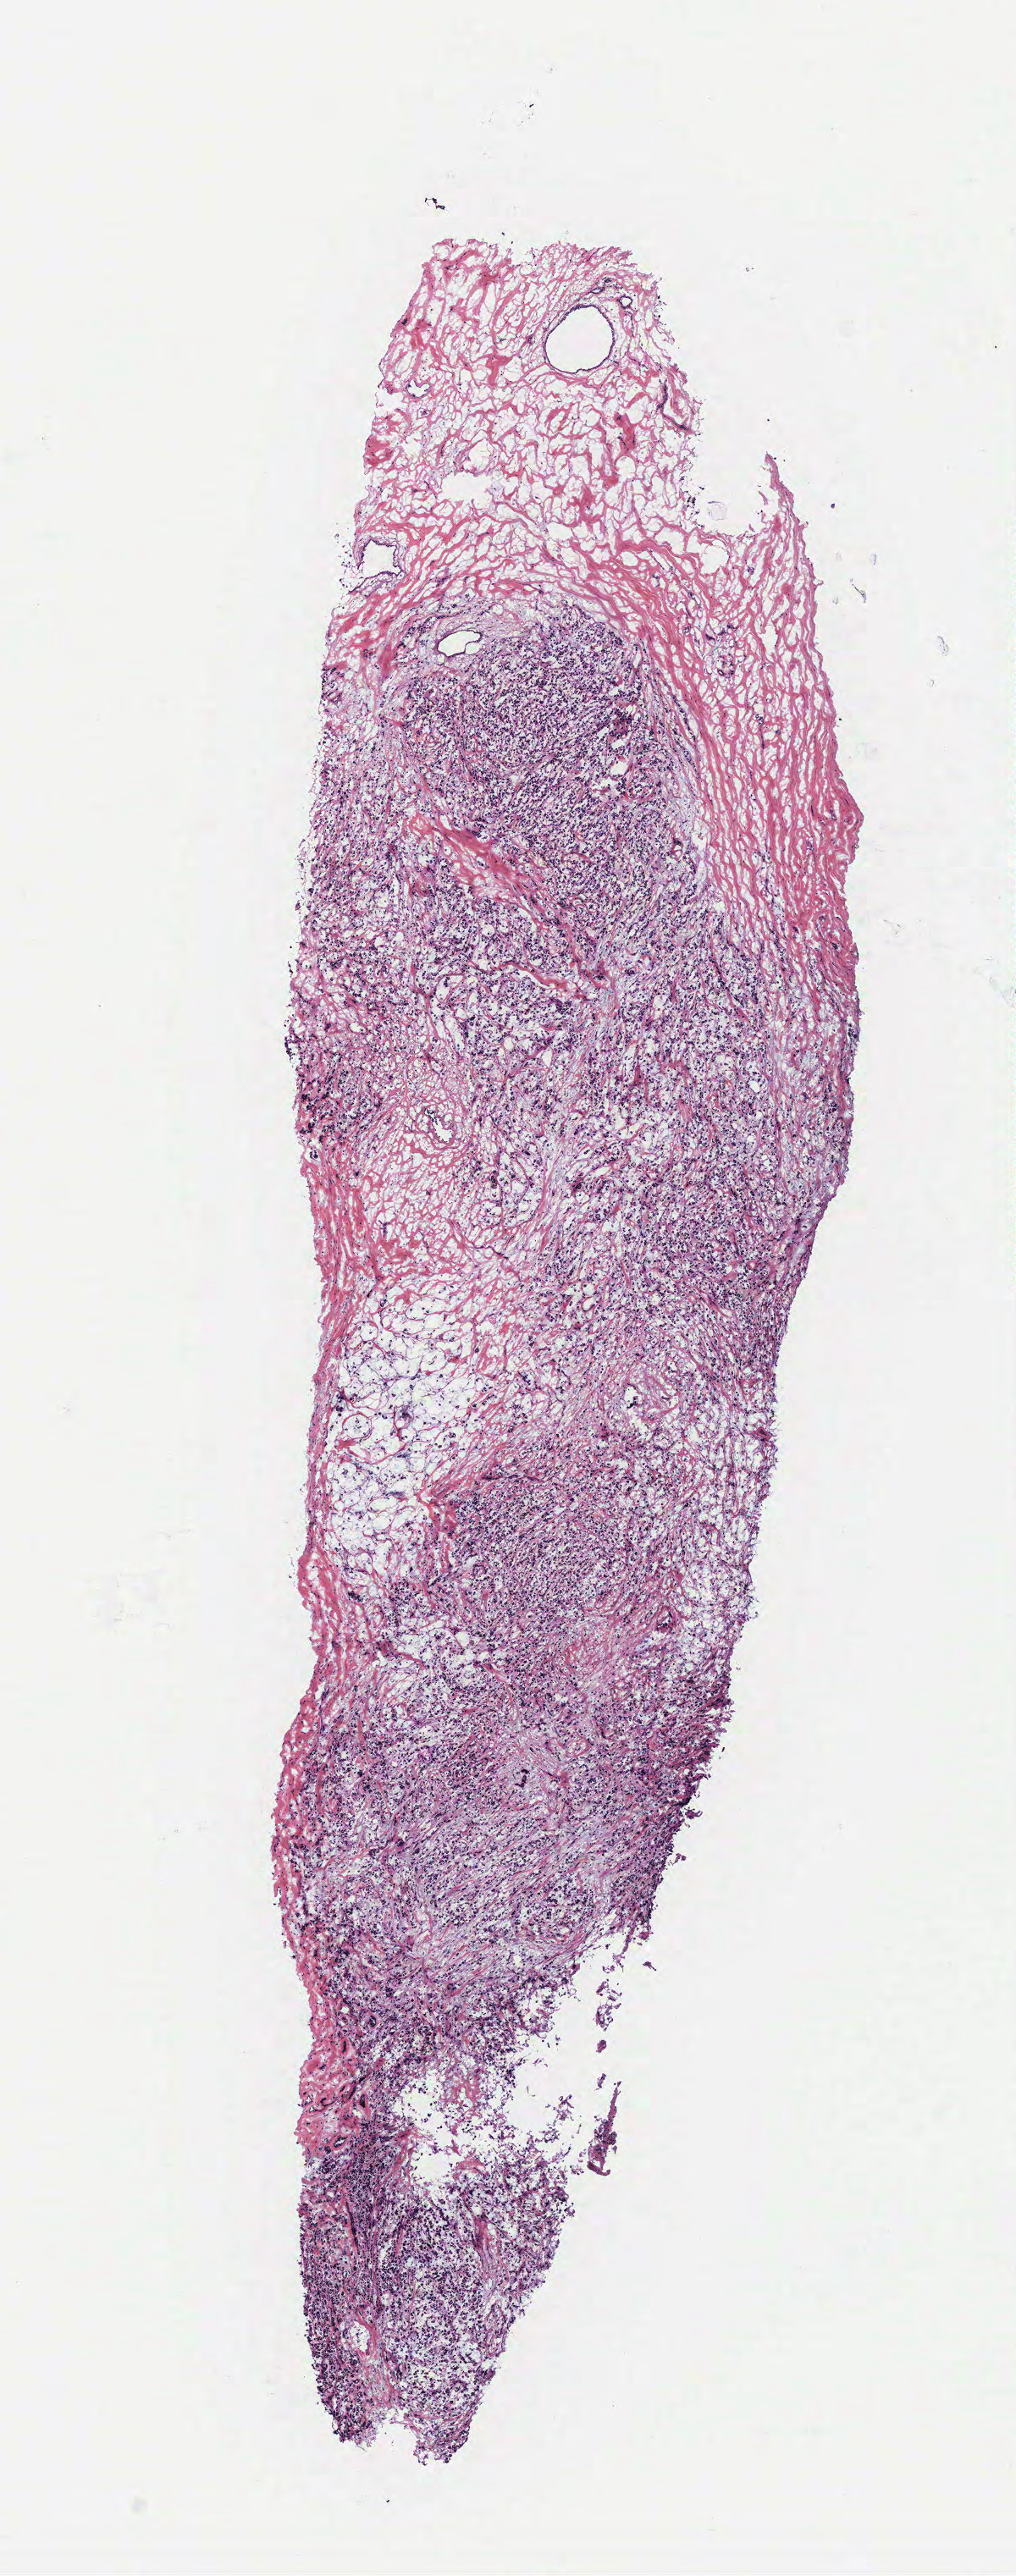
Digitized H&E-stained tissue section (whole slide), whole scanned area (about 4.8 x 12.2 mm, from a 40x scan) shown as a low-resolution overview, breast, tumour tissue. Patient: female, age 71 years.
- histologic diagnosis: Invasive lobular carcinoma
- AJCC pathologic stage: IIIA